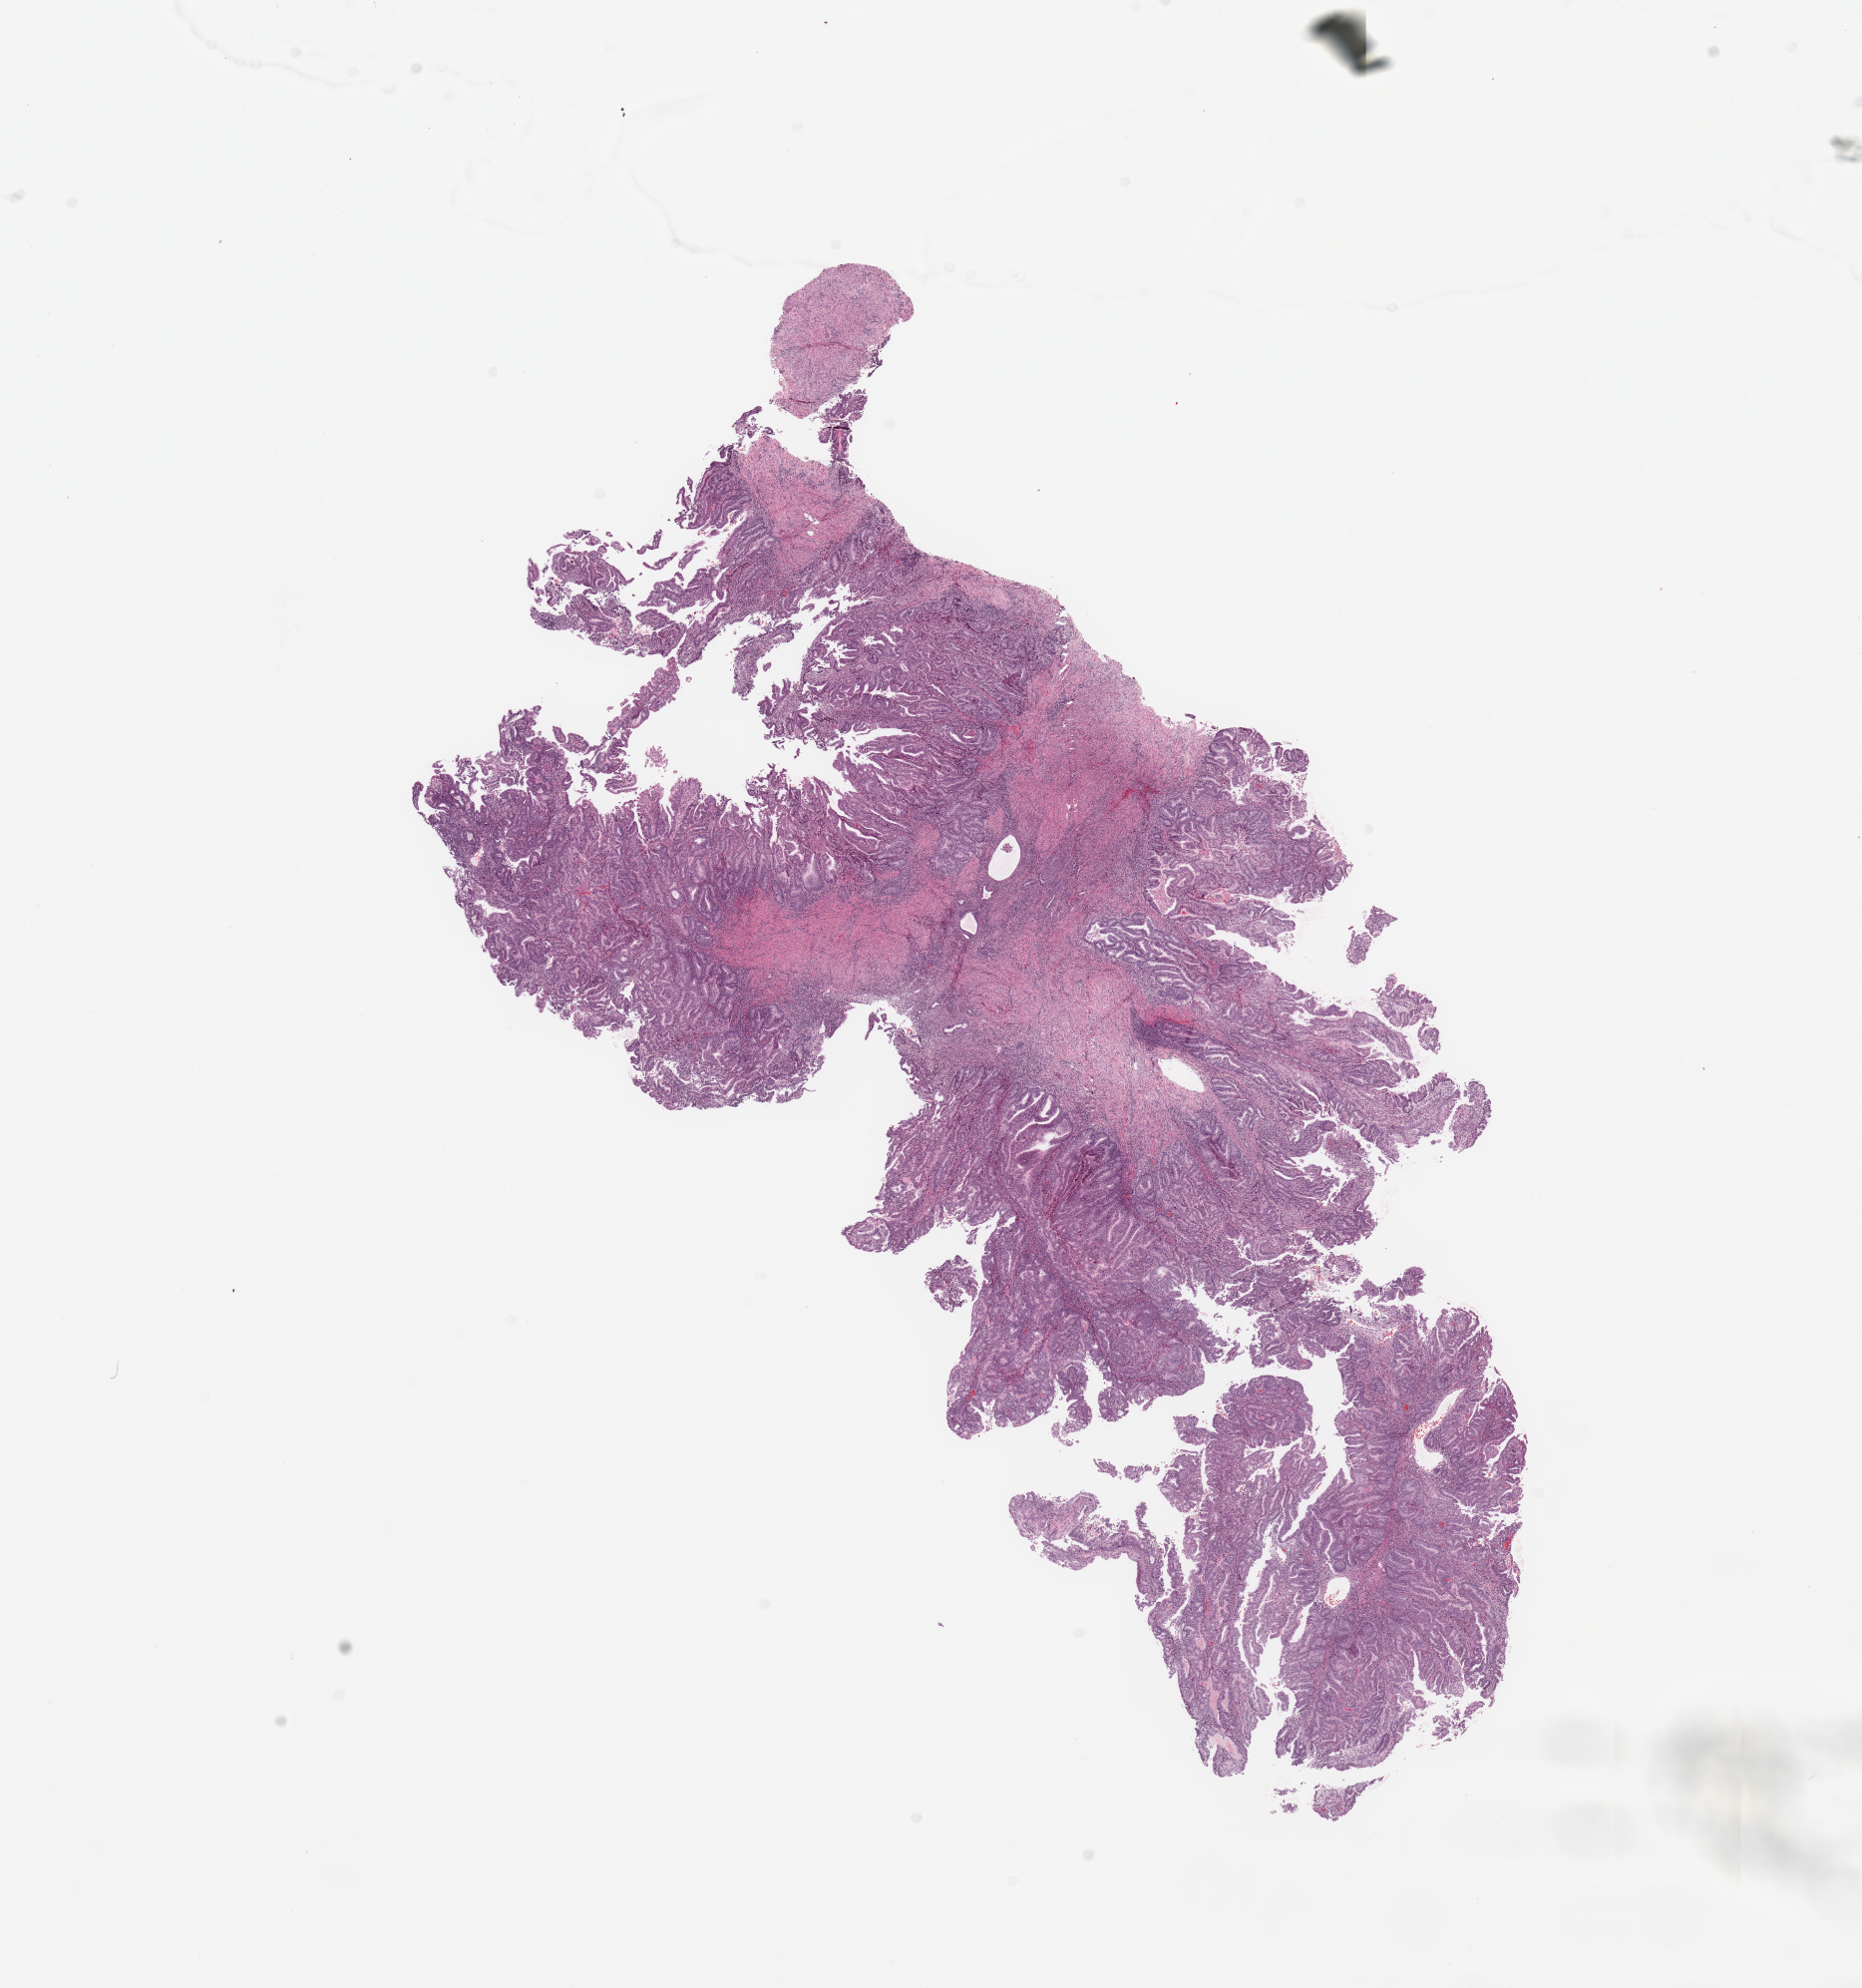
Digitized H&E tissue section (whole slide), shown as a low-resolution overview of the whole scanned area (about 14.8 x 15.8 mm, acquisition: 20x scan), tumour tissue sample, sampled site: uterus. Female, 56 y/o. Histologic grade: G1 (well differentiated). Composition of this section per pathologist review: tumour nuclei 80%, necrosis 0%.
- AJCC pathologic stage: I
- histologic diagnosis: Endometrioid adenocarcinoma, NOS